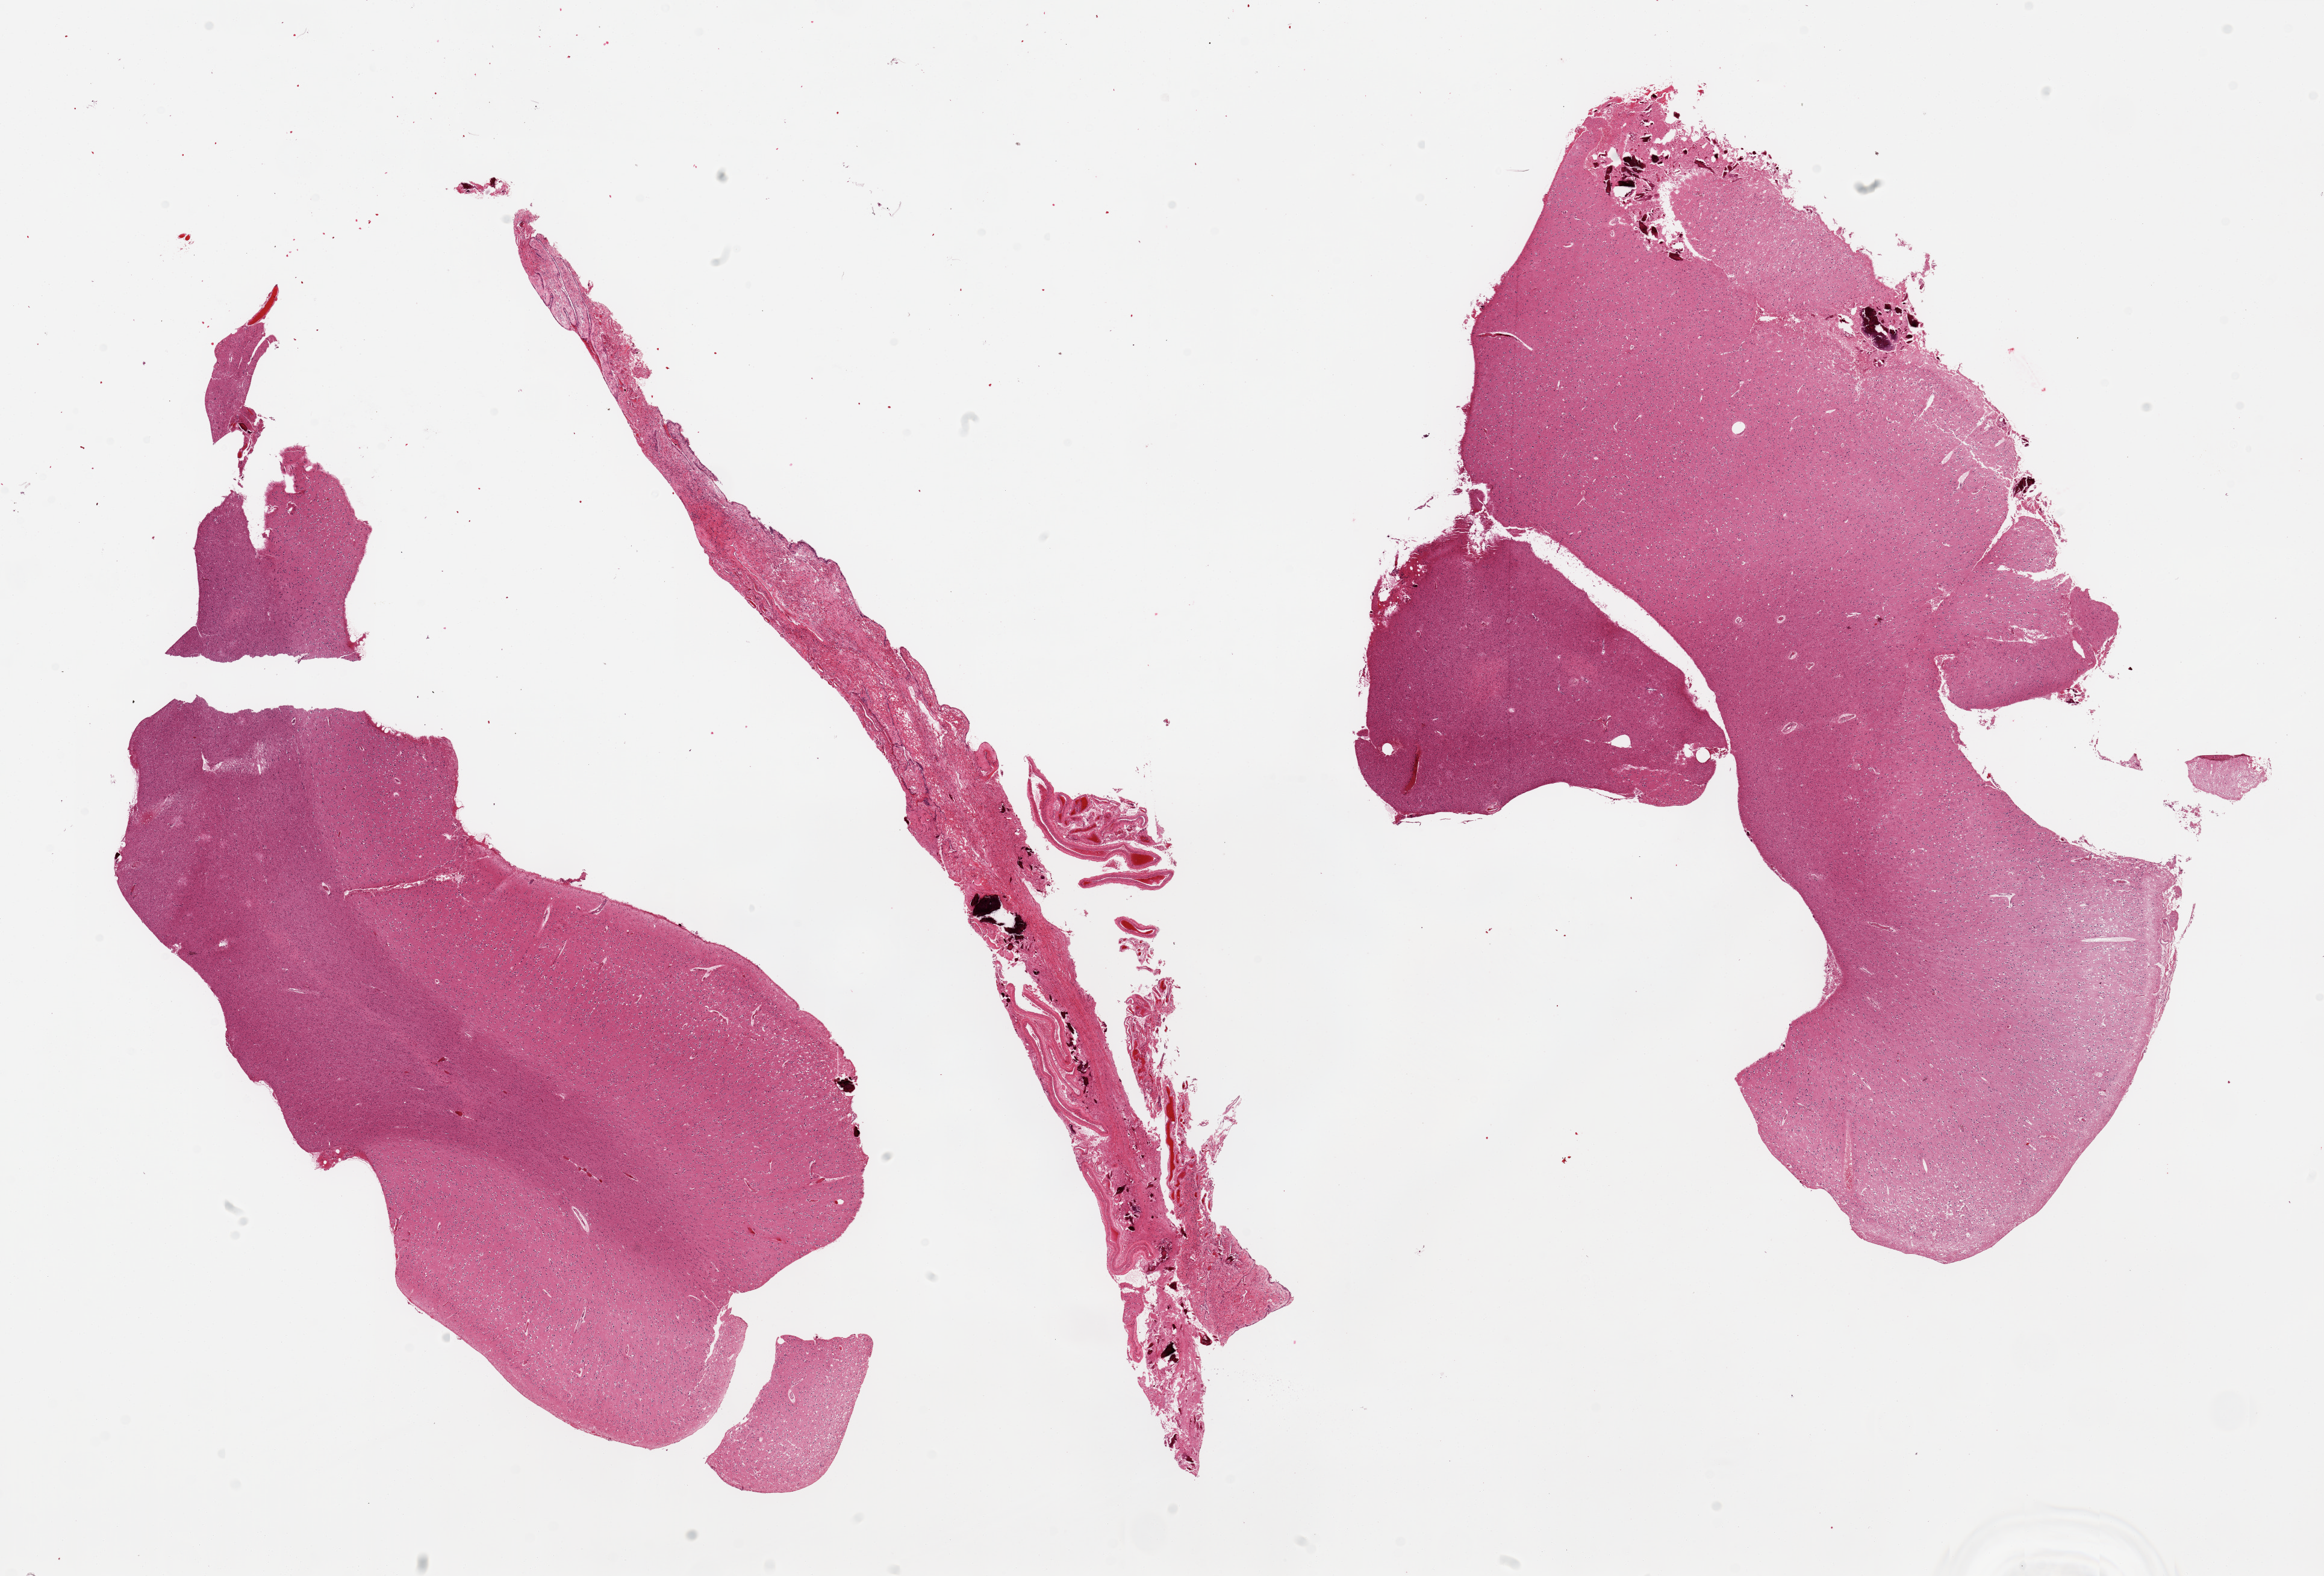
Digitized hematoxylin and eosin (H&E)-stained section, low-resolution overview of the scanned area, about 30.5 x 20.7 mm. PAXgene-fixed paraffin-embedded (PFPE) section. Section of cerebral cortex (target tissue). Donor tissue sample. Donor sex: male.
Reviewer comment on this tissue sample: 2 pieces and sliver of meninges all with artefactual bone fragments.